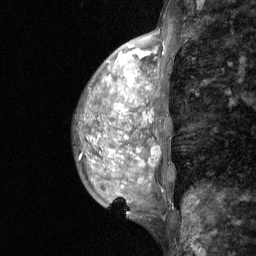
Breast MRI (dynamic contrast-enhanced), one sagittal slice; position 20 of 64 along the scan axis; dynamic contrast-enhanced study with each time point stored as its own series, time point 2 of 3 at this slice position (early post-contrast, ordered by acquisition time); 1.5 T; TE 4.8 ms, TR 27 ms; 2 mm slice thickness; 256 × 256 image matrix, field of view 200 × 200 mm. Female patient, age 36 years. From the clinical record (not read from this slice): setting: breast cancer imaged before/during neoadjuvant chemotherapy; receptor status: HR-positive, HER2-negative.
Structures marked on this image (semi-automatic segmentation, software-assisted and operator-edited):
- analysis volume of interest (the breast-tissue region the enhancement analysis was run in; not a lesion): bounding box <76,84,175,210> (left, top, right, bottom; pixels)
- tumour enhancement mask (voxels above the 90 % enhancement threshold inside the analysis volume of interest): <118,105,142,166>